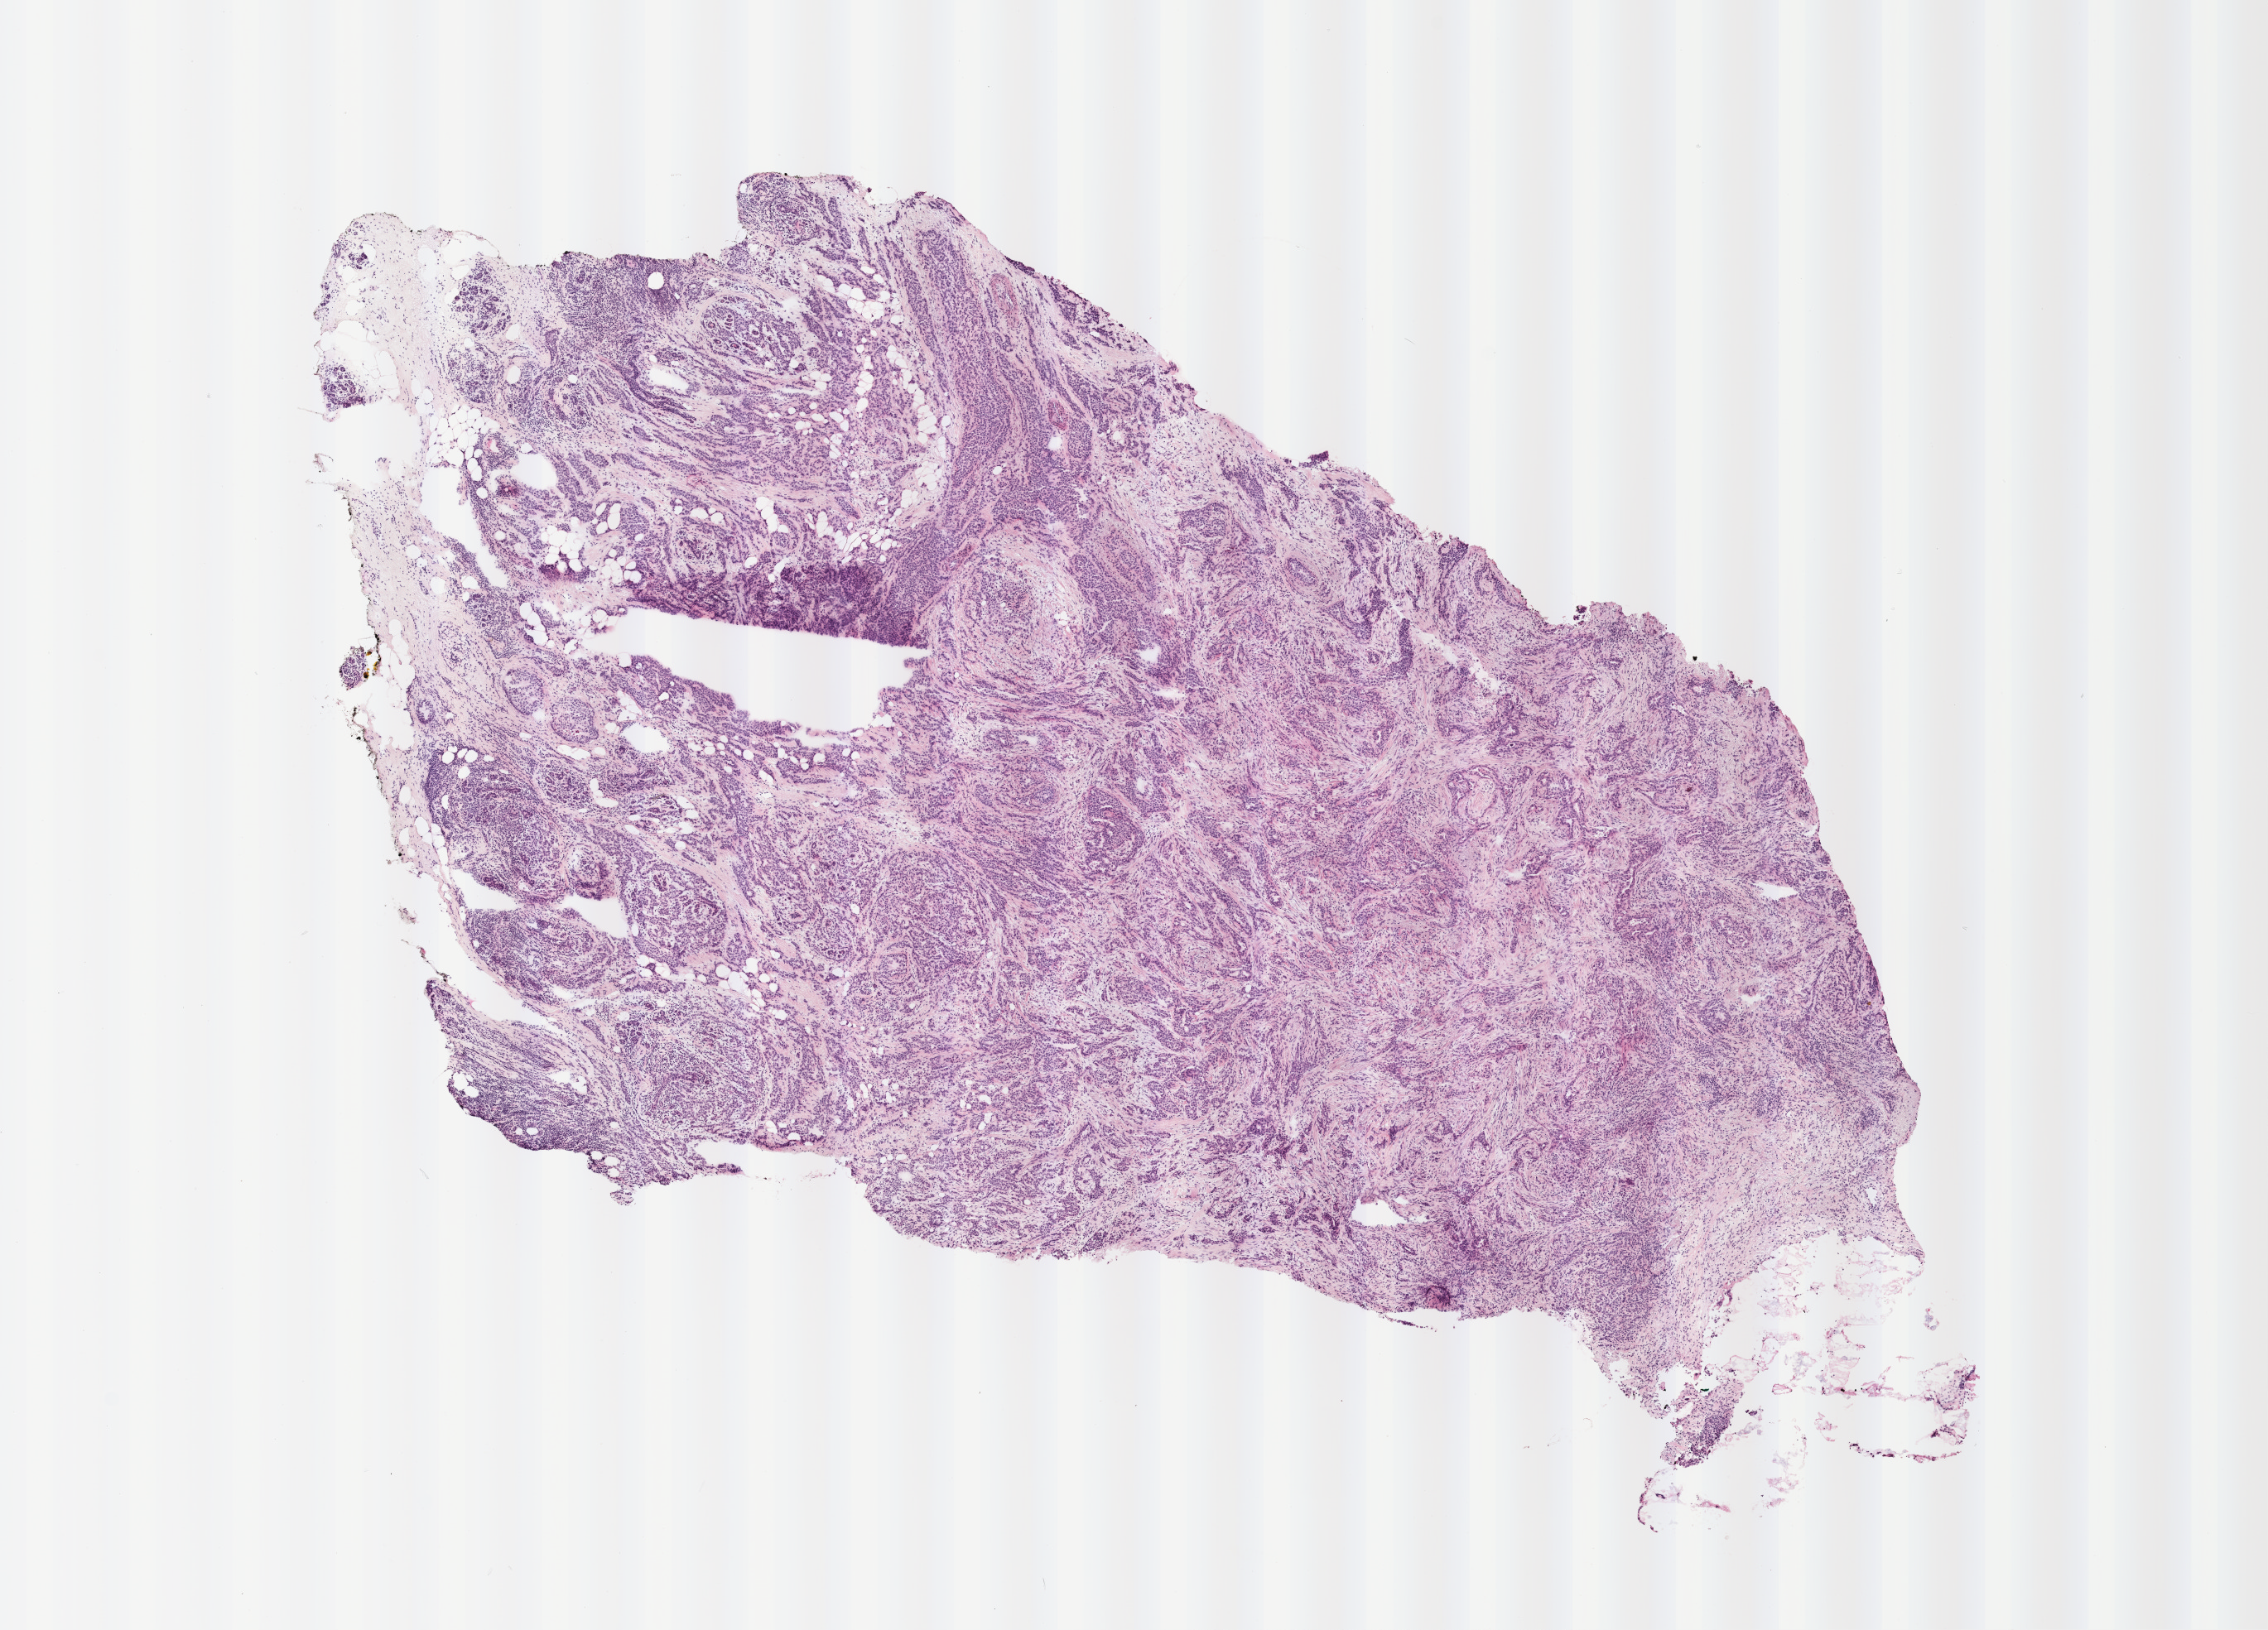
Digitized H&E-stained section, a low-resolution overview of the entire scanned area, about 11.0 x 7.9 mm. Cryosection. Primary tumor. Anatomic site: breast (right). Female, age 52 years at initial diagnosis. Pathologist review of this section (percent, as recorded): tumor cells 63%, tumor nuclei 65%, stromal cells 25%, necrosis 2%, normal cells 10%. Inflammatory infiltration, as recorded: lymphocyte infiltration 5%, monocyte infiltration 2%, neutrophil infiltration 2%.
- diagnosis: Infiltrating duct carcinoma, NOS
- section: top of the tissue portion